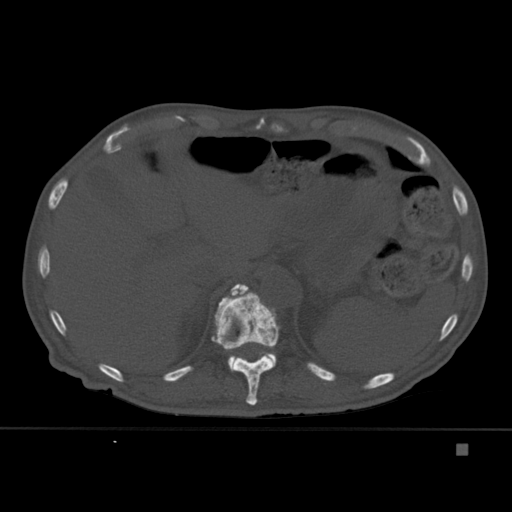
CT including the spine, one axial slice. Position 214 of 451 along the scan axis. Bone window (W 1800 / L 400 HU). 1.5 mm slice thickness. 512 × 512 image matrix, field of view 378 × 378 mm. Patient: male, 75 years. From the clinical record (not read from this slice): primary cancer: prostate.
Outlined on this slice (semi-automatic segmentation, software-assisted and operator-edited):
- T11 vertebra: box from (x=211, y=284) to (x=281, y=405) px
- T12 vertebra: (x=227, y=284)–(x=277, y=372)